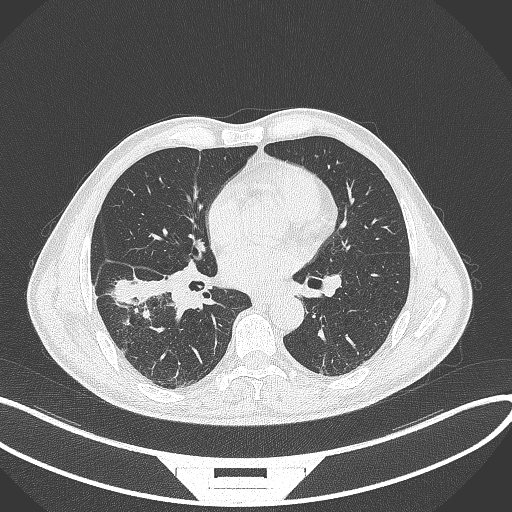
Chest CT, one axial slice. Position 171 of 364 along the scan axis. Lung window (W 1500 / L -600 HU). 512 × 512 image matrix, field of view 400 × 400 mm. Patient: male, 58 years. Case-level facts recorded for this patient, not image findings: clinical TNM (as recorded): T3 N0 M0.
Structures marked on this image (bounding box drawn by a radiologist):
- lung tumour (recorded histology: squamous cell carcinoma): bounding box (x1, y1, x2, y2) in pixels: (115, 277, 170, 307)